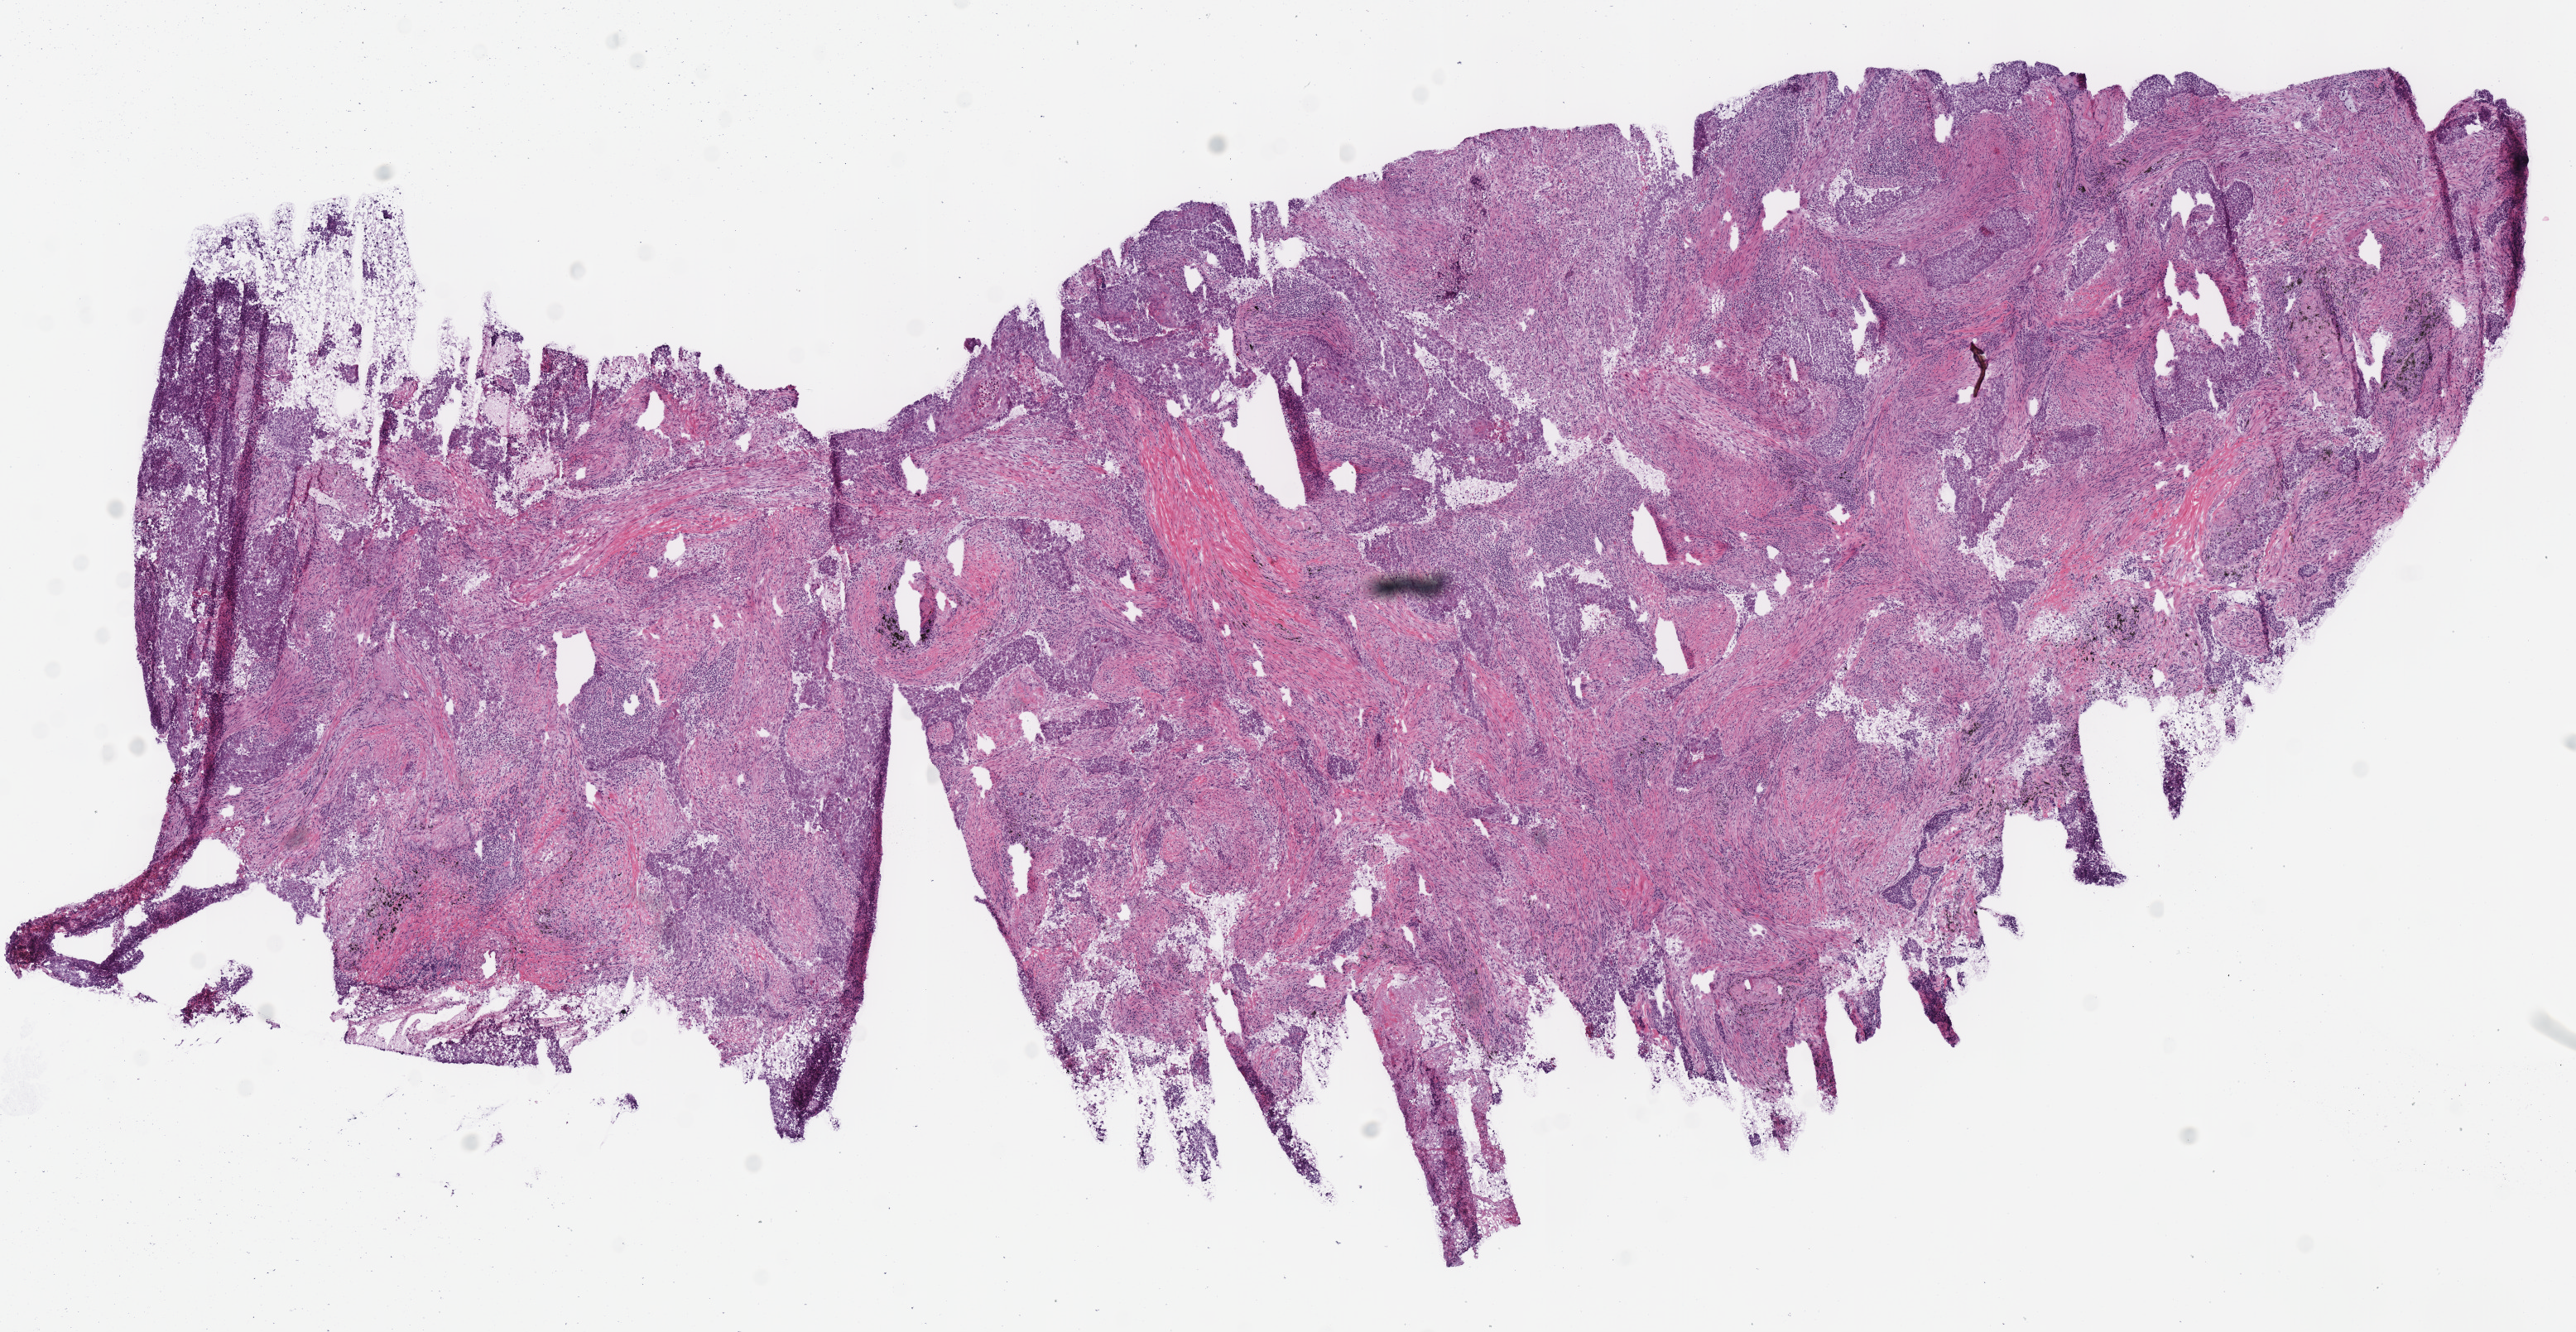
Whole-slide histology image, H&E-stained, whole scanned area (about 12.2 x 6.3 mm, slide scanned at 40x) shown as a low-resolution overview; frozen section from the top of the tissue portion; primary tumour sample from the lung. Female patient; age at initial diagnosis 72 years. Pathologist review of this section (percent, as recorded): tumour cells 95%, tumour nuclei 65%.
Pathologic diagnosis: Squamous cell carcinoma, NOS (lower lobe, lung).